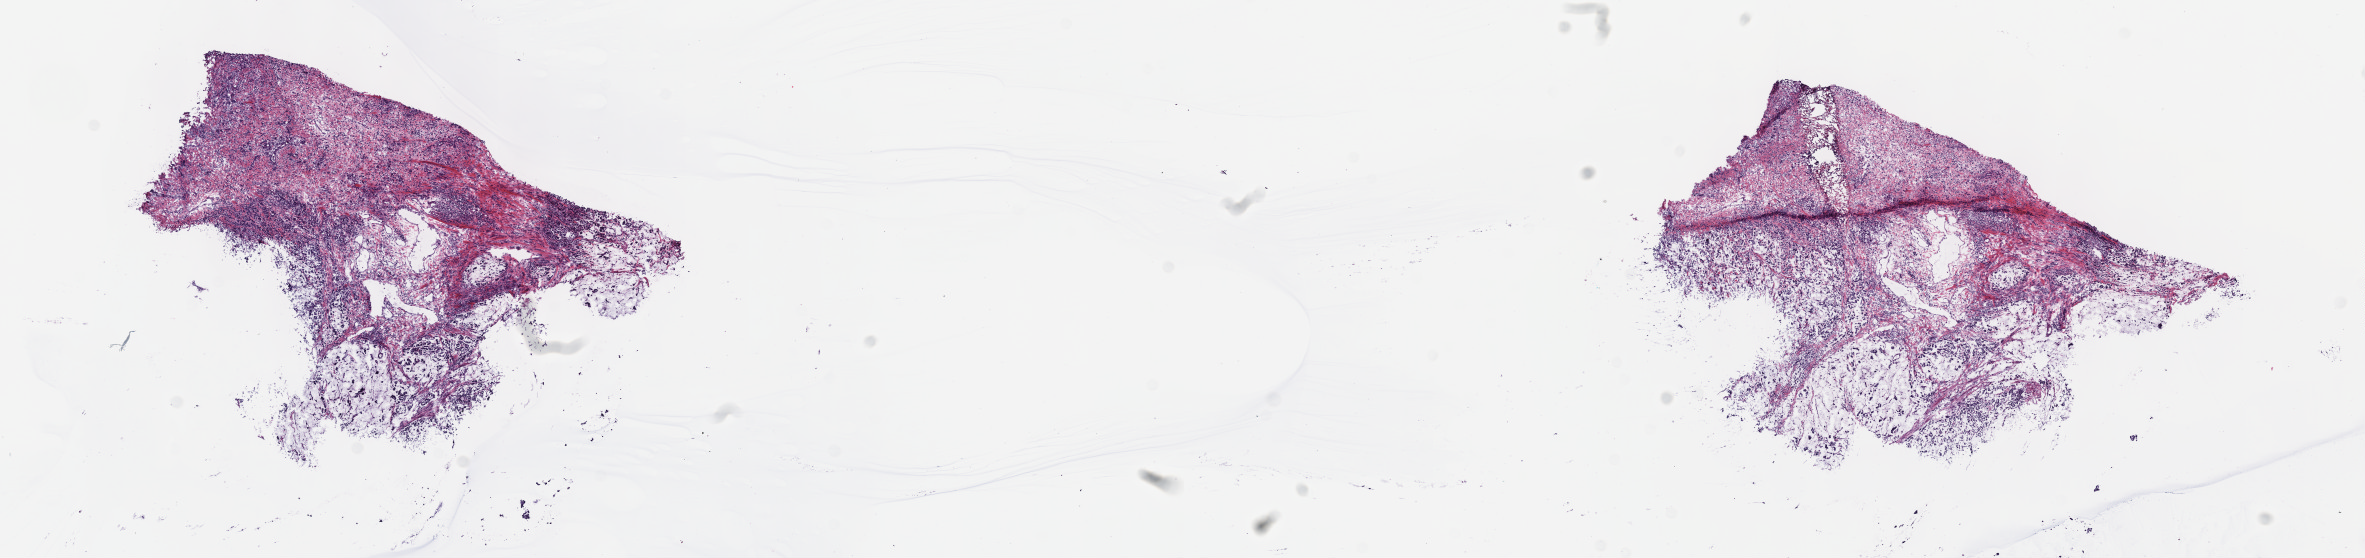
Digitized Hematoxylin and eosin (H&E) stained tissue section (whole slide), whole scanned area (about 19.1 x 4.5 mm, acquisition: 40x scan) shown as a low-resolution overview. Frozen section from the top of the tissue portion. Sample: primary tumour, esophagus. Male patient; age at initial diagnosis 55 years.
Diagnosis: Adenocarcinoma, NOS.